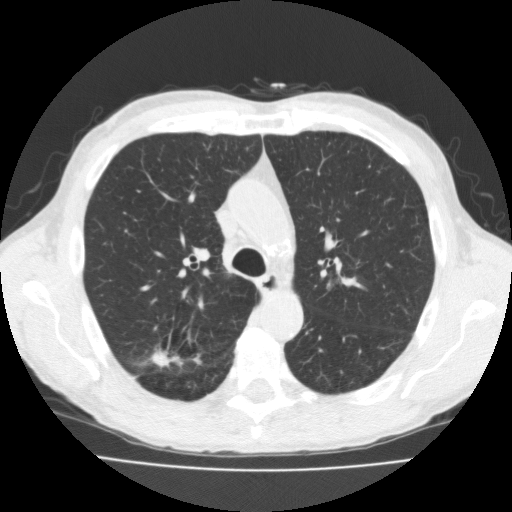
Low-dose screening chest CT, one axial slice. Position 122 of 181 along the scan axis. 120 kVp. Lung window (W 1500 / L -600 HU). 2 mm slice thickness. 512 × 512 image matrix, field of view 350 × 350 mm.
Structures marked on this image (expert manual segmentation):
- lesion 1 (tumor, upper lobe of right lung): box from (x=152, y=350) to (x=179, y=367) px